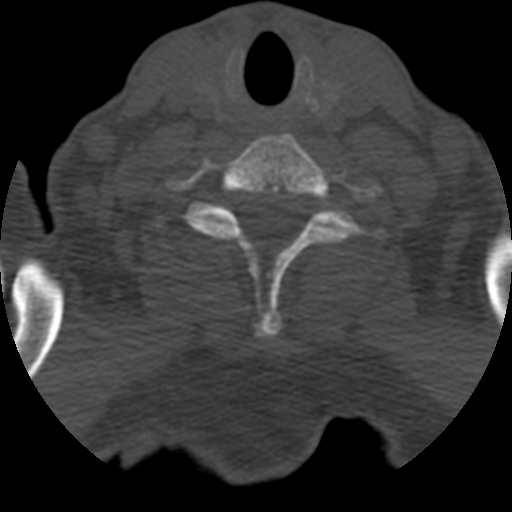
CT including the spine, one axial slice. One of 3 acquisitions stored at this slice position. Bone window (W 1800 / L 400 HU). 512 × 512 image matrix, field of view 160 × 160 mm. Patient age 55 years. Case-level facts recorded for this patient, not image findings: primary cancer: colon; vertebrae with lytic lesions (as recorded): T12, L1, L5.
Structures marked on this image (semi-automatic segmentation, software-assisted and operator-edited):
- T1 vertebra: box from (x=152, y=201) to (x=390, y=253) px